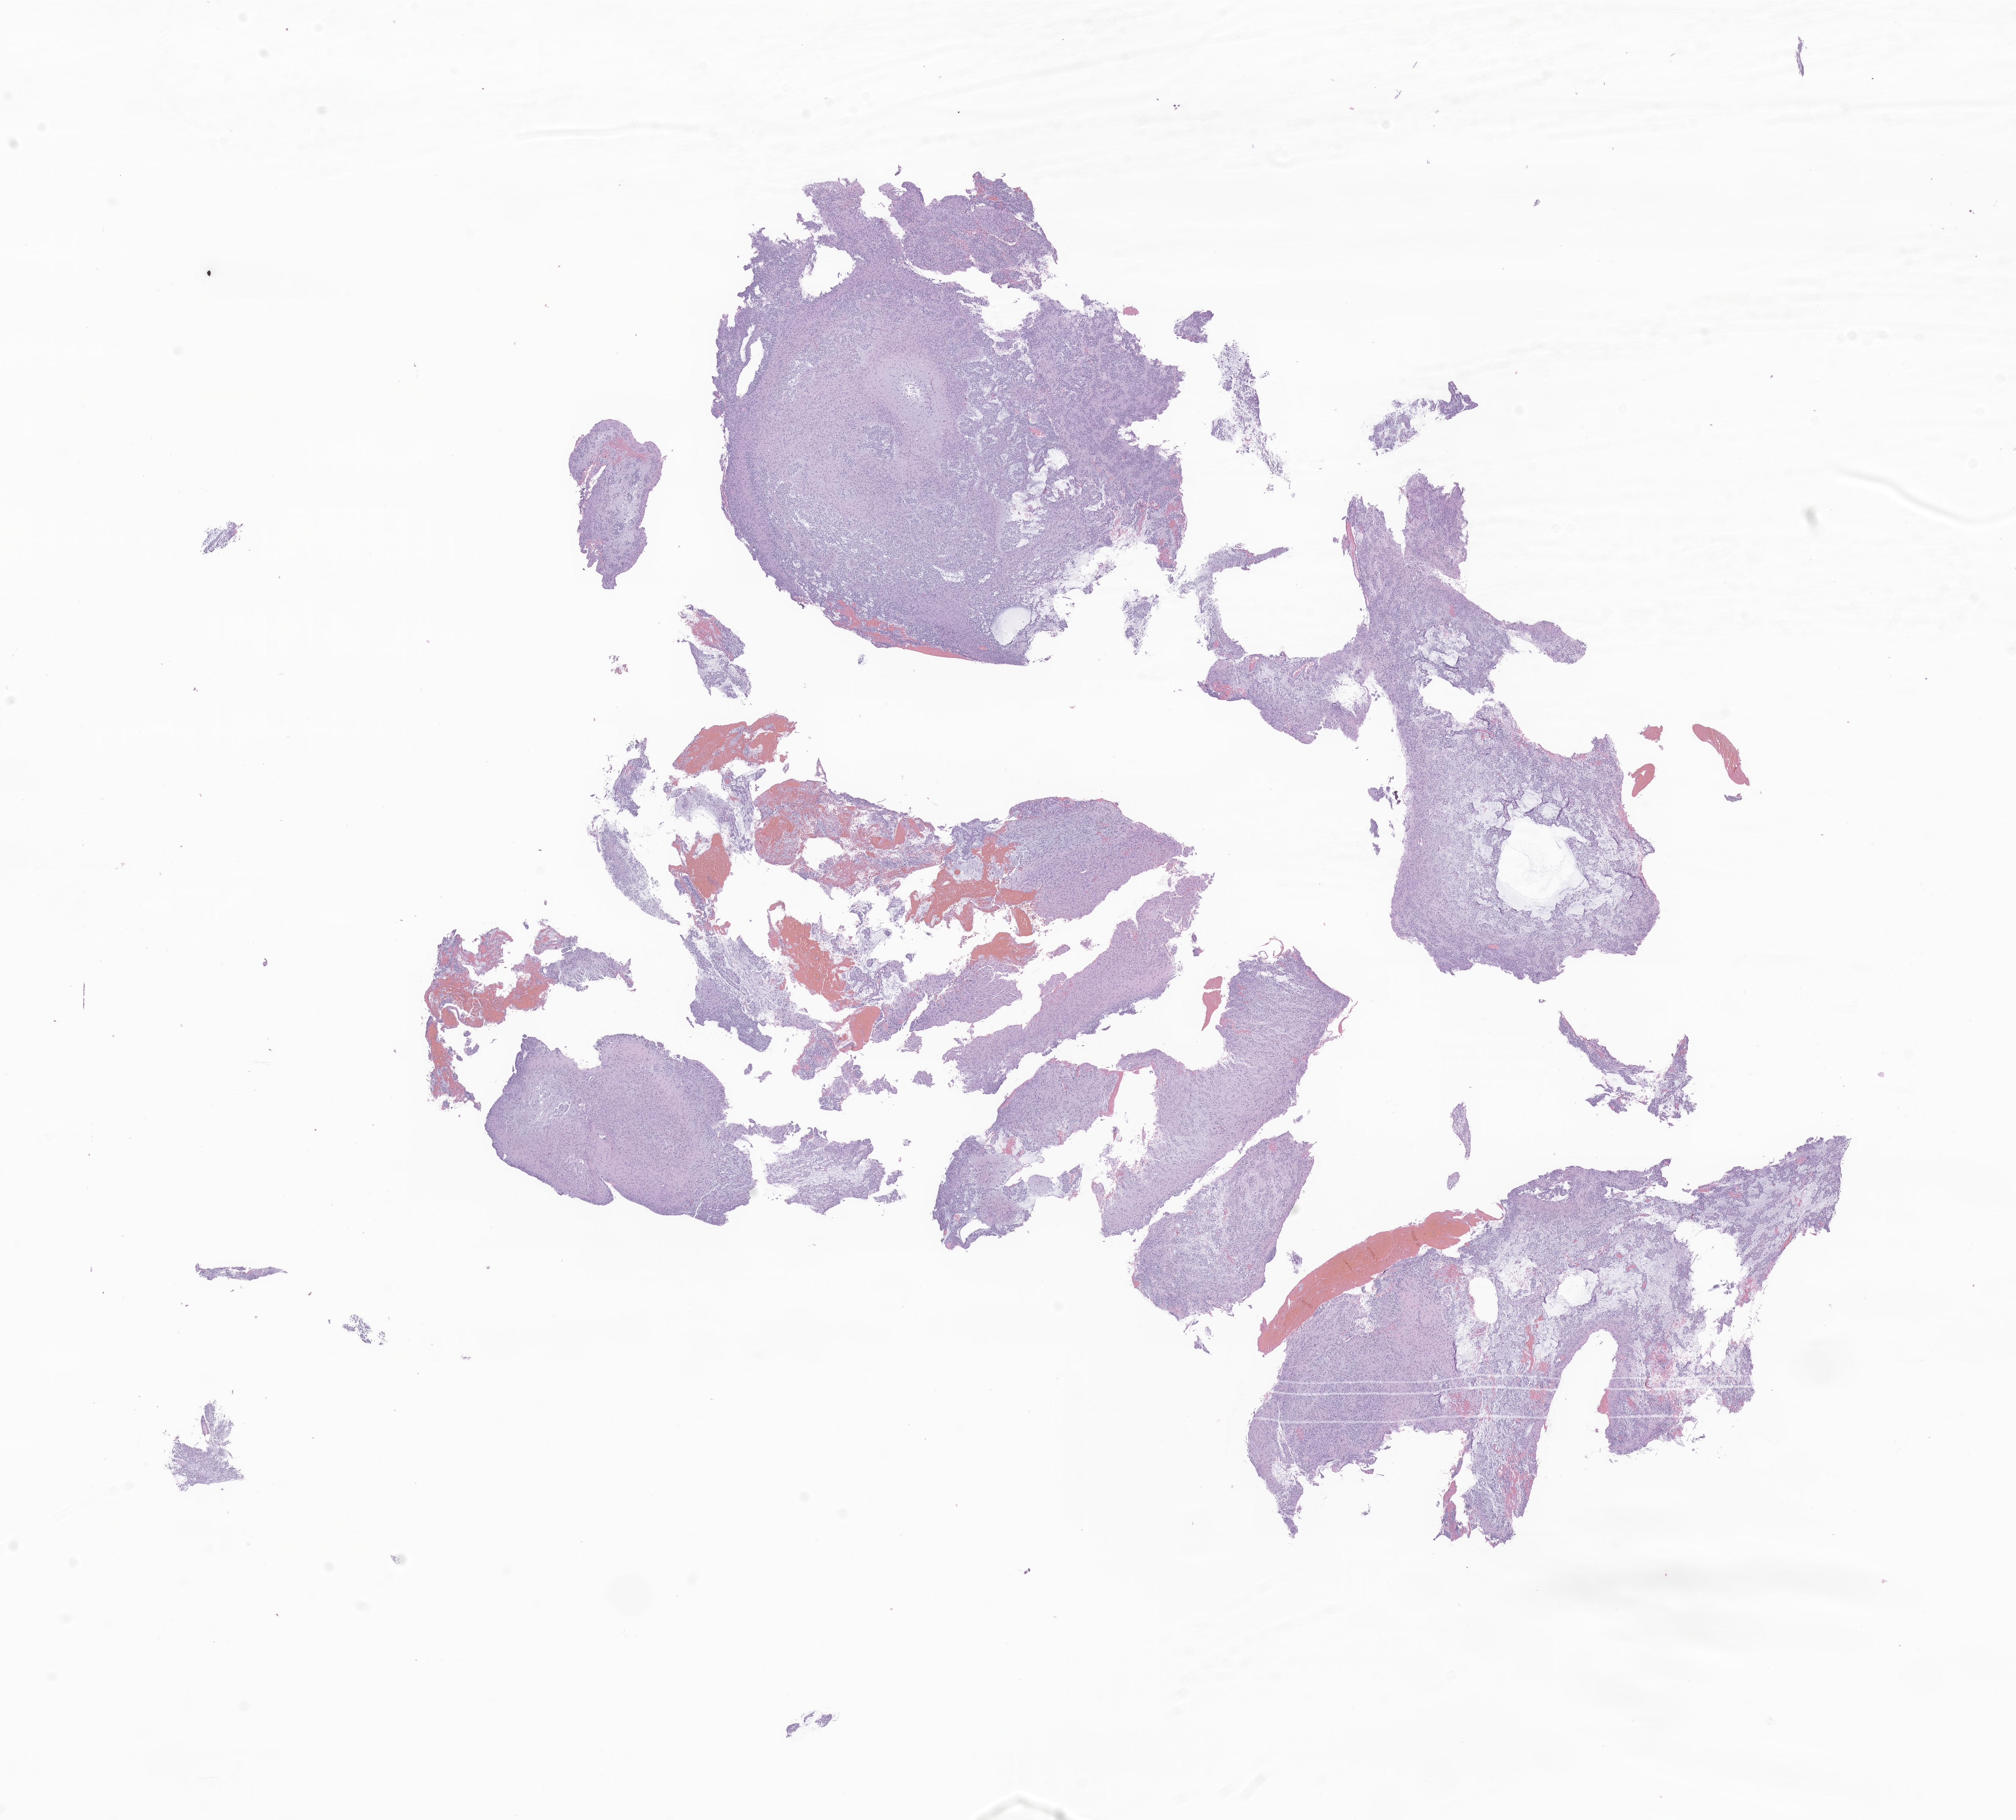
Whole-slide image, haematoxylin and eosin stain of tumor tissue from the brain — shown as a low-resolution overview of the whole scanned area (about 22.6 x 20.4 mm); formalin-fixed paraffin-embedded section. Patient female; age 137 months (11 years 5 months).
Diagnosis (ICD-O-3 morphology term): Oligoastrocytoma, NOS.